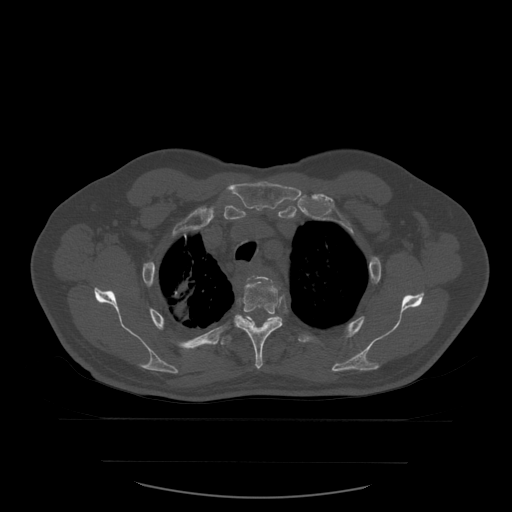
CT including the spine, one axial slice; position 441 of 590 along the scan axis; bone window (W 1800 / L 400 HU); 512 × 512 image matrix, field of view 479 × 479 mm. Patient age 71 years. From the clinical record (not read from this slice): primary cancer: lung; vertebrae with lytic lesions (as recorded): T1, T2, L5, S1.
Structures marked on this image (semi-automatically segmented with operator editing):
- T3 vertebra: bounding box (x1, y1, x2, y2) in pixels: (250, 276, 272, 283)
- T4 vertebra: (234, 276, 283, 370)
- T5 vertebra: (220, 322, 255, 346)